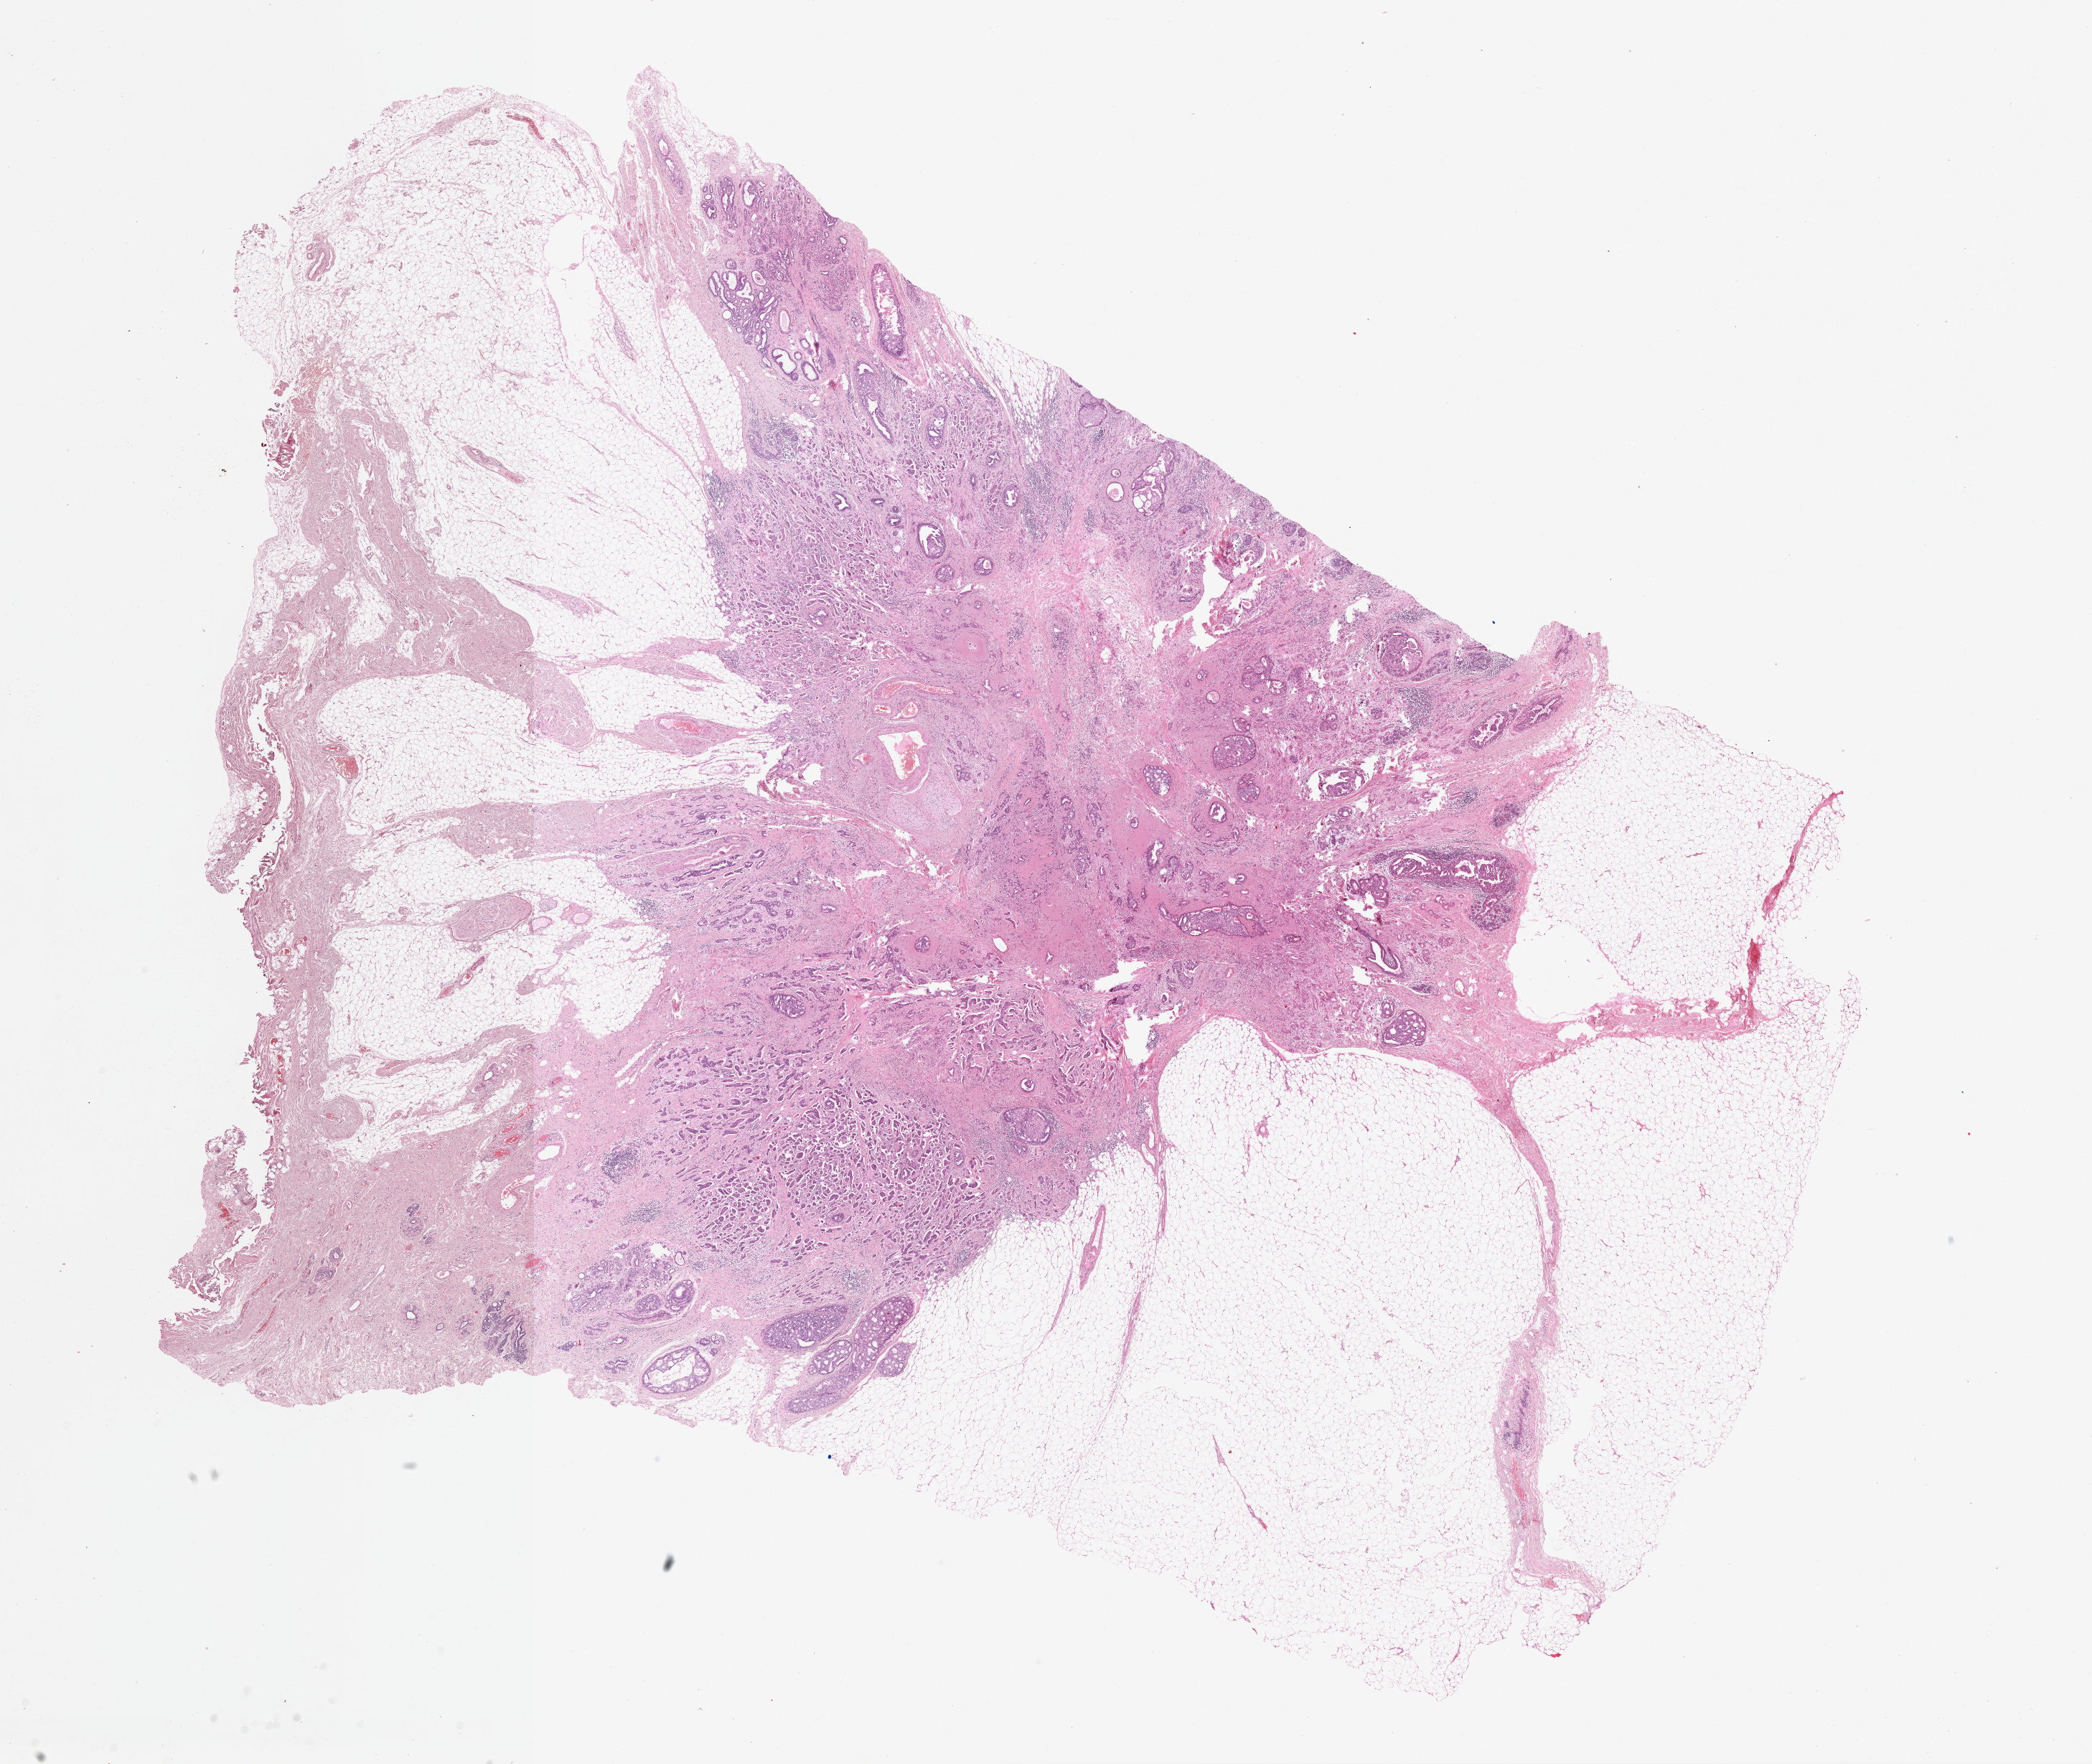
Hematoxylin and eosin (H&E) stained whole-slide image — a low-resolution overview of the entire scanned area, about 23.0 x 19.4 mm (slide scanned at 40x); formalin-fixed paraffin-embedded (FFPE) diagnostic section; sample: primary tumour, breast. Patient: female, age at initial diagnosis 49 years.
AJCC pathologic stage: IIIA (7th edition). Lymph nodes positive (case pathology): 2 of 16 examined. Pathologic diagnosis: Infiltrating duct carcinoma, NOS.